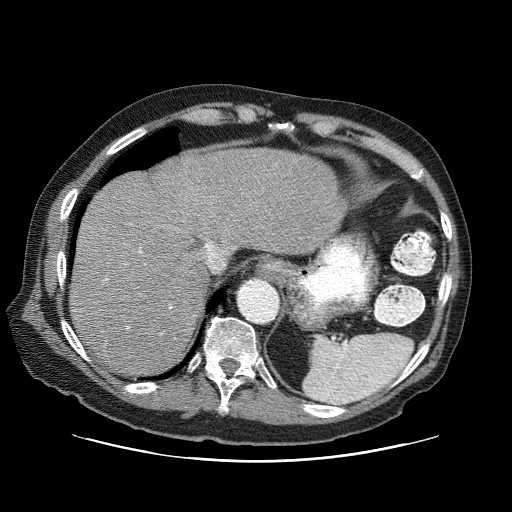
Contrast-enhanced abdominal CT (liver protocol), one axial slice; position 60 of 87 along the scan axis; 120 kVp; one of 3 acquisitions stored at this slice position; soft-tissue window (W 400 / L 40 HU); 2.5 mm slice thickness; 512 × 512 image matrix, field of view 400 × 400 mm. Case-level facts recorded for this patient, not image findings: diagnosis: hepatocellular carcinoma (patient treated with transarterial chemoembolisation; whether this scan precedes or follows treatment is not stated here); TNM stage (as recorded): Stage-IIIA; Child-Pugh class: A; tumour differentiation: well differentiated; tumour nodularity: multinodular.
Annotated regions visible in this slice (semi-automatically segmented with operator editing):
- liver parenchyma outside the tumour (the mass and vessels are separate outlines, so this box may not span the whole liver): bounding box [x1, y1, x2, y2] px = [70, 148, 346, 376]
- liver vessels: [74, 249, 172, 328]